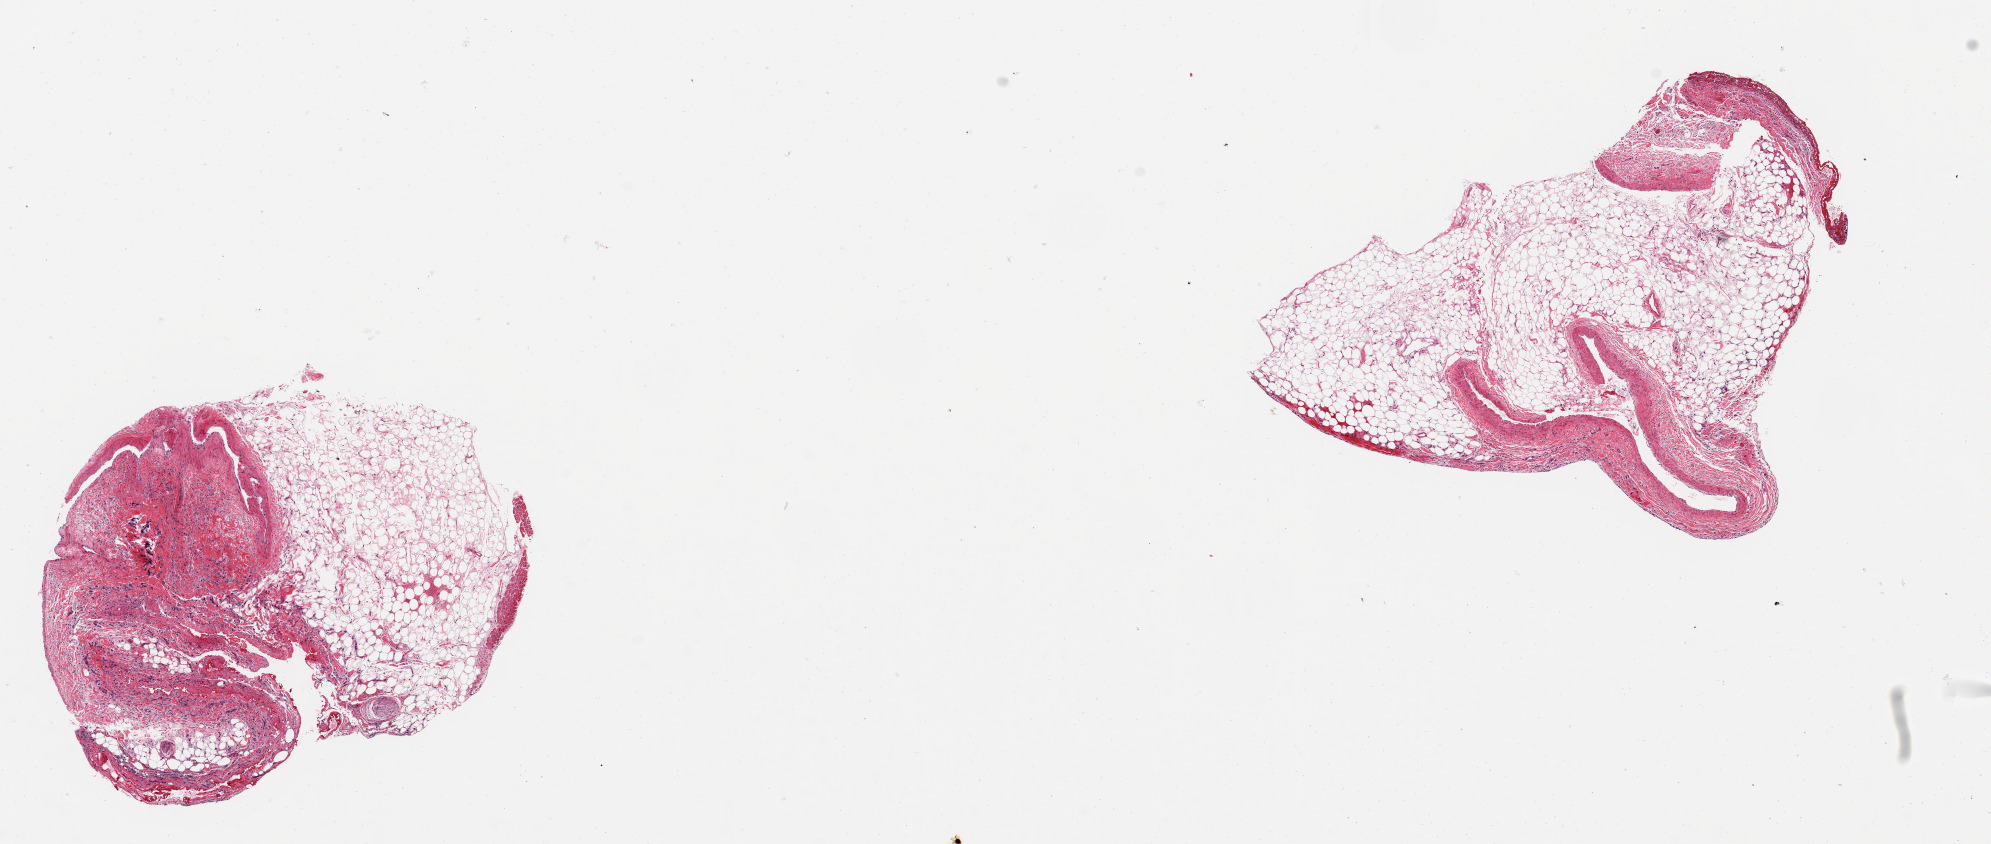
Whole-slide image, haematoxylin and eosin stain, shown as a low-resolution overview of the whole scanned area (about 15.8 x 6.7 mm); PAXgene-fixed paraffin-embedded (PFPE) section; section of coronary artery (target tissue); donor tissue sample. Male donor.
Review note (as recorded): 2 pieces; portions of veins with large amounts of fat and fibrous tissue [>60%].